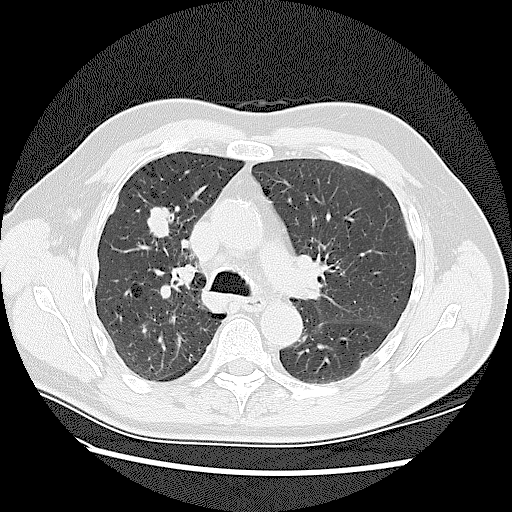
Low-dose screening chest CT, one axial slice. 120 kVp. Lung window (W 1500 / L -600 HU). 2.5 mm slice thickness. 512 × 512 image matrix.
Structures marked on this image (expert manual segmentation):
- lesion 1 (tumor, upper lobe of right lung): bounding box (x1, y1, x2, y2) in pixels: (147, 207, 171, 238)